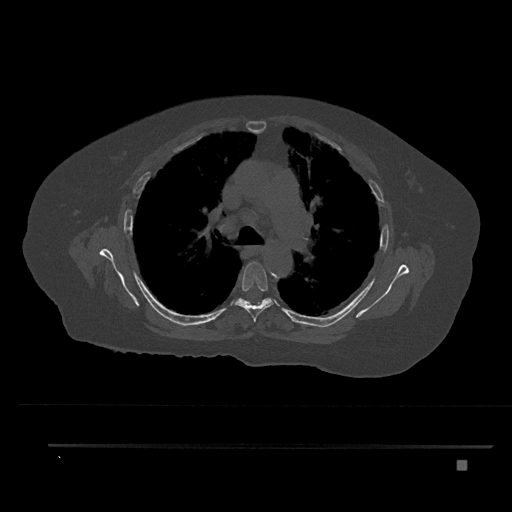
CT including the spine, one axial slice; slice 560 of 797 in the series (ordered by position); 120 kVp; bone window (W 1800 / L 400 HU); 512 × 512 image matrix, field of view 437 × 437 mm. Patient: female, 76 years. Case-level facts recorded for this patient, not image findings: primary cancer: lung.
Outlined on this slice (semi-automatically segmented with operator editing):
- T5 vertebra: bounding box <234,261,274,322> (left, top, right, bottom; pixels)
- T6 vertebra: <235,298,273,306>